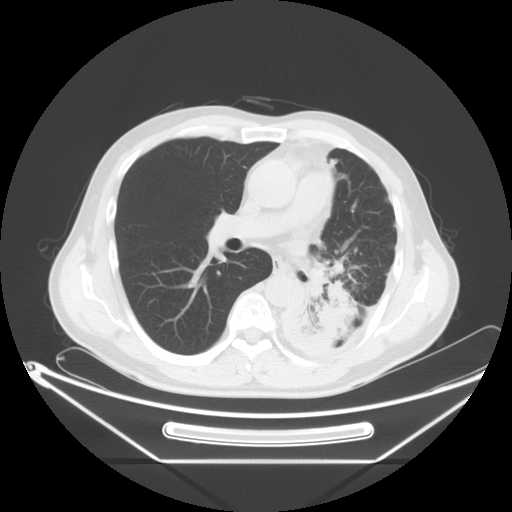
Chest CT, one axial slice. Slice 35 of 63 in the series (ordered by position). Reconstruction kernel STANDARD. 120 kVp. Lung window (W 1500 / L -600 HU). 5 mm slice thickness. 512 × 512 image matrix. Patient: male, 60 years. From the clinical record (not read from this slice): clinical TNM (as recorded): T4 N1 M1.
Outlined on this slice (bounding box drawn by a radiologist):
- lung tumour (recorded histology: adenocarcinoma): bounding box <302,248,361,353> (left, top, right, bottom; pixels)